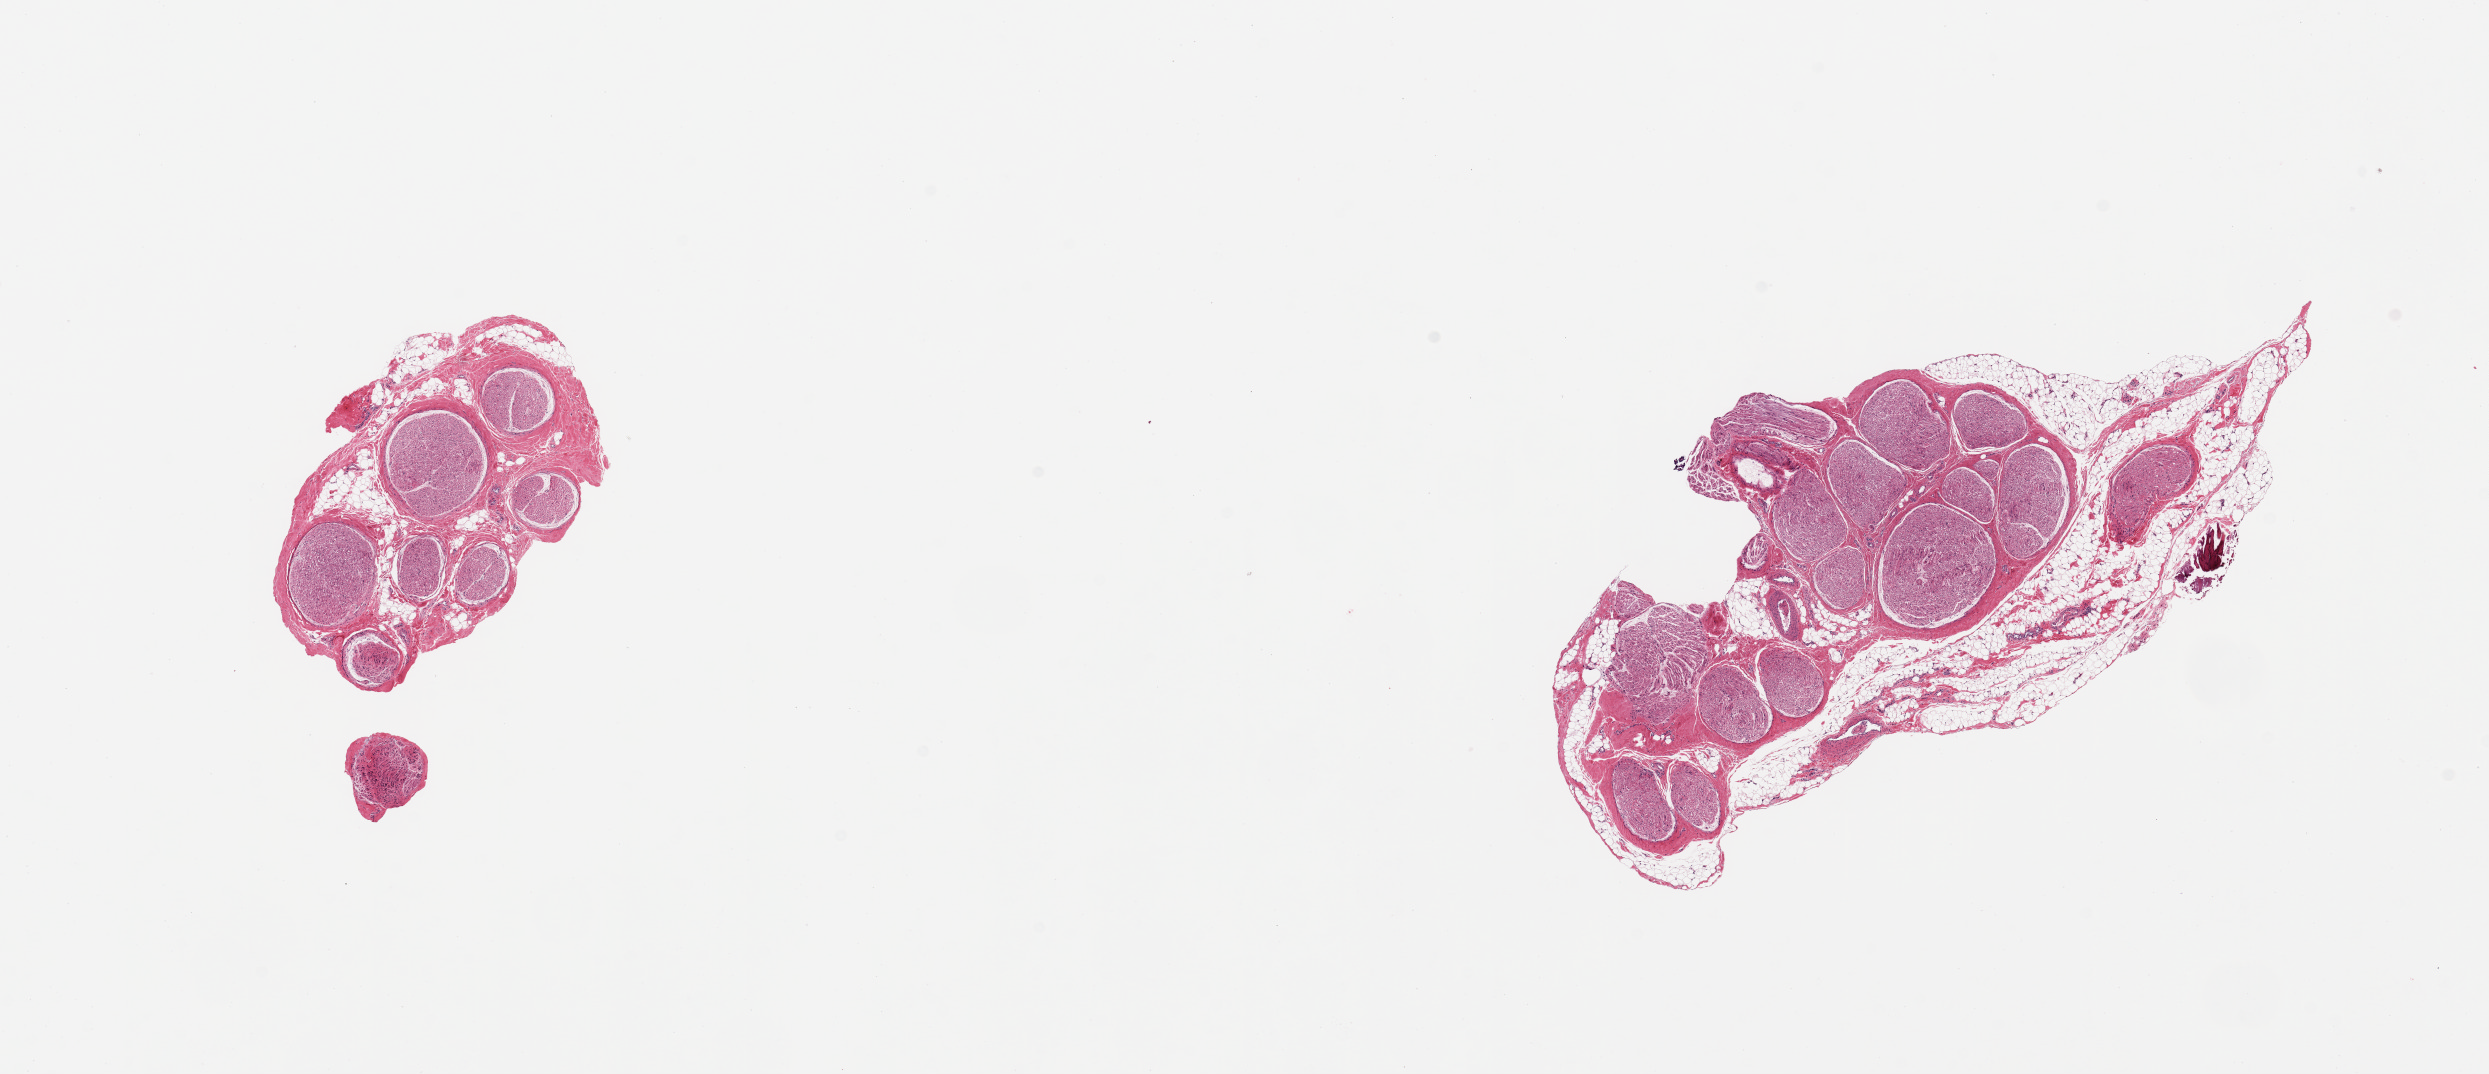
Hematoxylin and eosin (H&E) whole-slide image, brightfield — whole scanned area (about 19.7 x 8.5 mm, from a 20x scan) shown as a low-resolution overview; PAXgene-fixed, paraffin-embedded tissue; sampled site (target tissue): tibial nerve; donor tissue sample. Donor sex: male.
Pathologist's review note for this sample: 2 pieces; up to 30% external fat; focus of extraneous bone fragments.